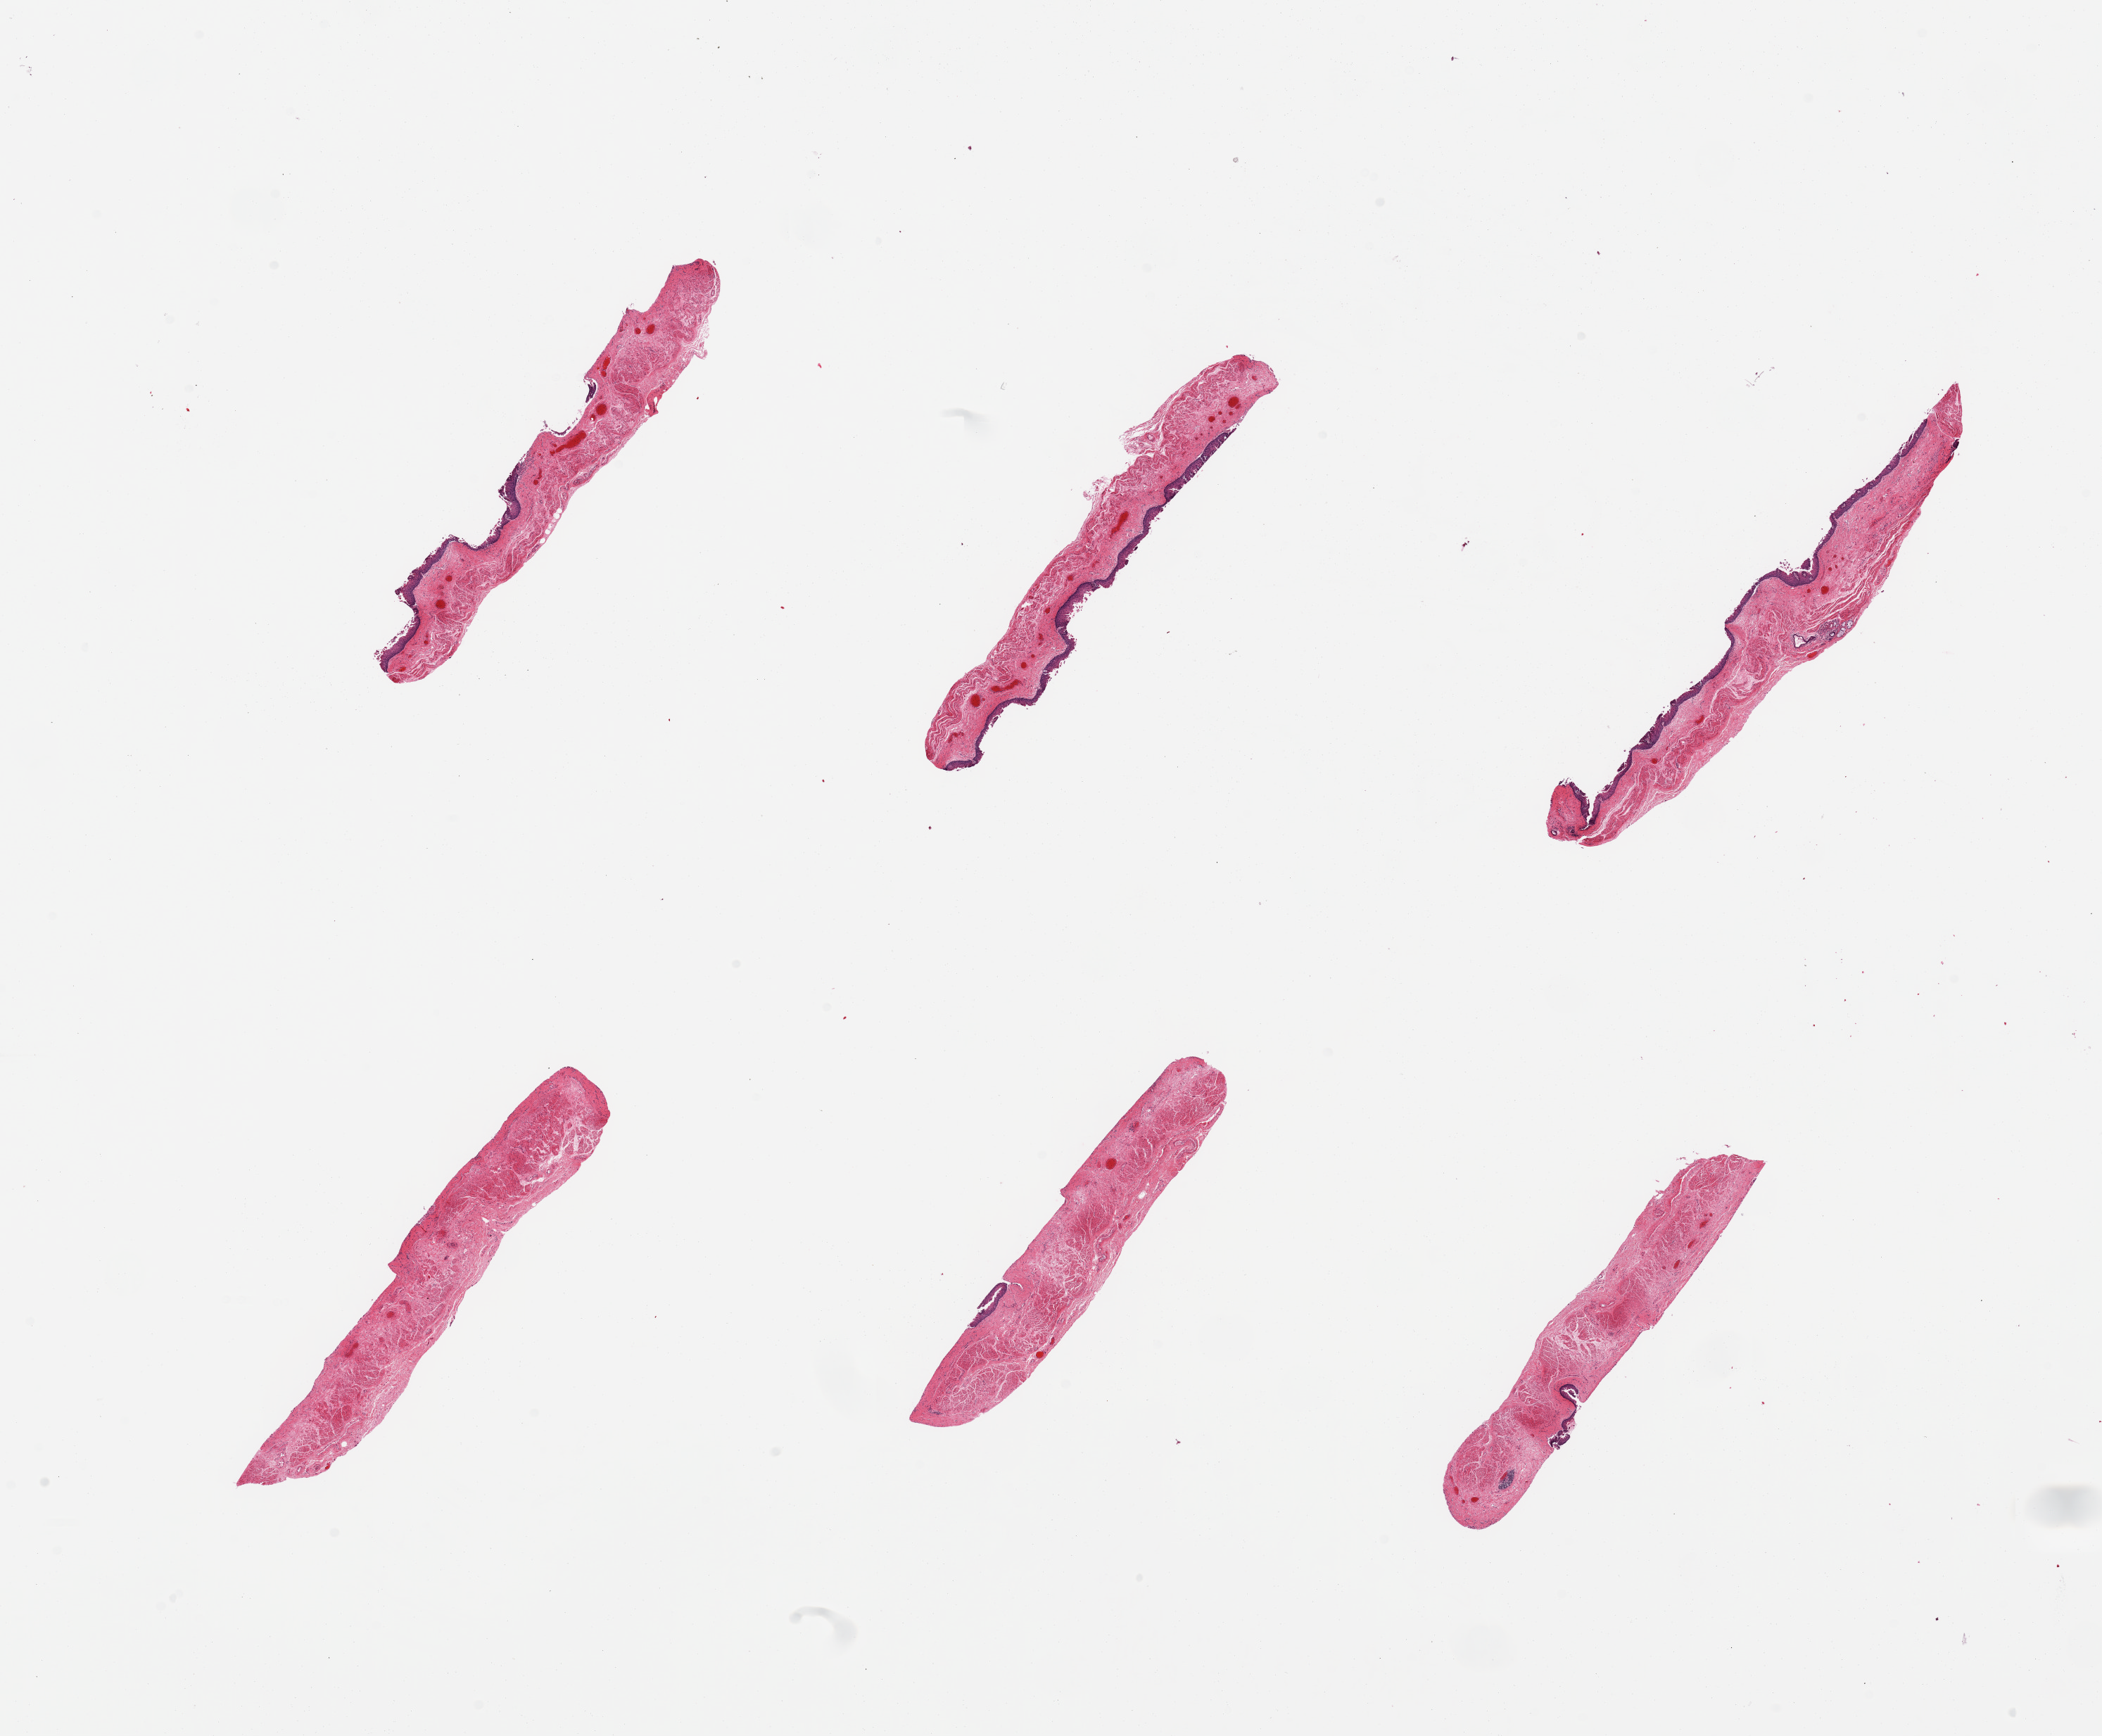
Digitized haematoxylin and eosin-stained section, low-resolution overview of the scanned area, about 23.6 x 19.5 mm (from a 20x scan), PAXgene-fixed, paraffin-embedded tissue, sampled site (target tissue): esophageal mucous membrane, tissue donor sample. Donor sex: male.
Pathologist's review note for this sample: 6 pieces; surface desquamation.